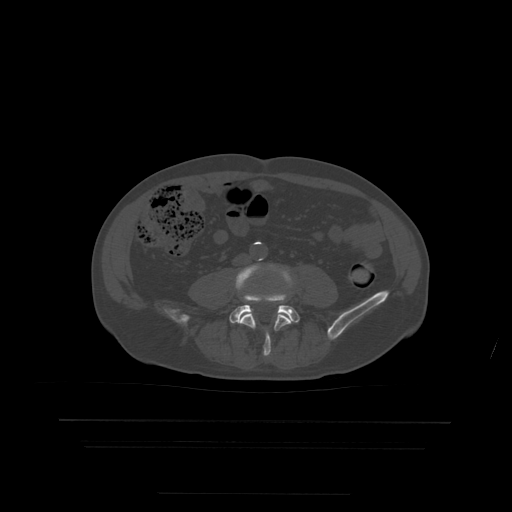
CT including the spine, one axial slice; position 85 of 522 along the scan axis; bone window (W 1800 / L 400 HU); 1.25 mm slice thickness; 512 × 512 image matrix, field of view 436 × 436 mm. Patient age 68 years. Case-level facts recorded for this patient, not image findings: primary cancer: urothelial.
Annotated regions visible in this slice (semi-automatically segmented with operator editing):
- L4 vertebra: box from (x=236, y=264) to (x=293, y=357) px
- L5 vertebra: (x=230, y=294)–(x=300, y=323)